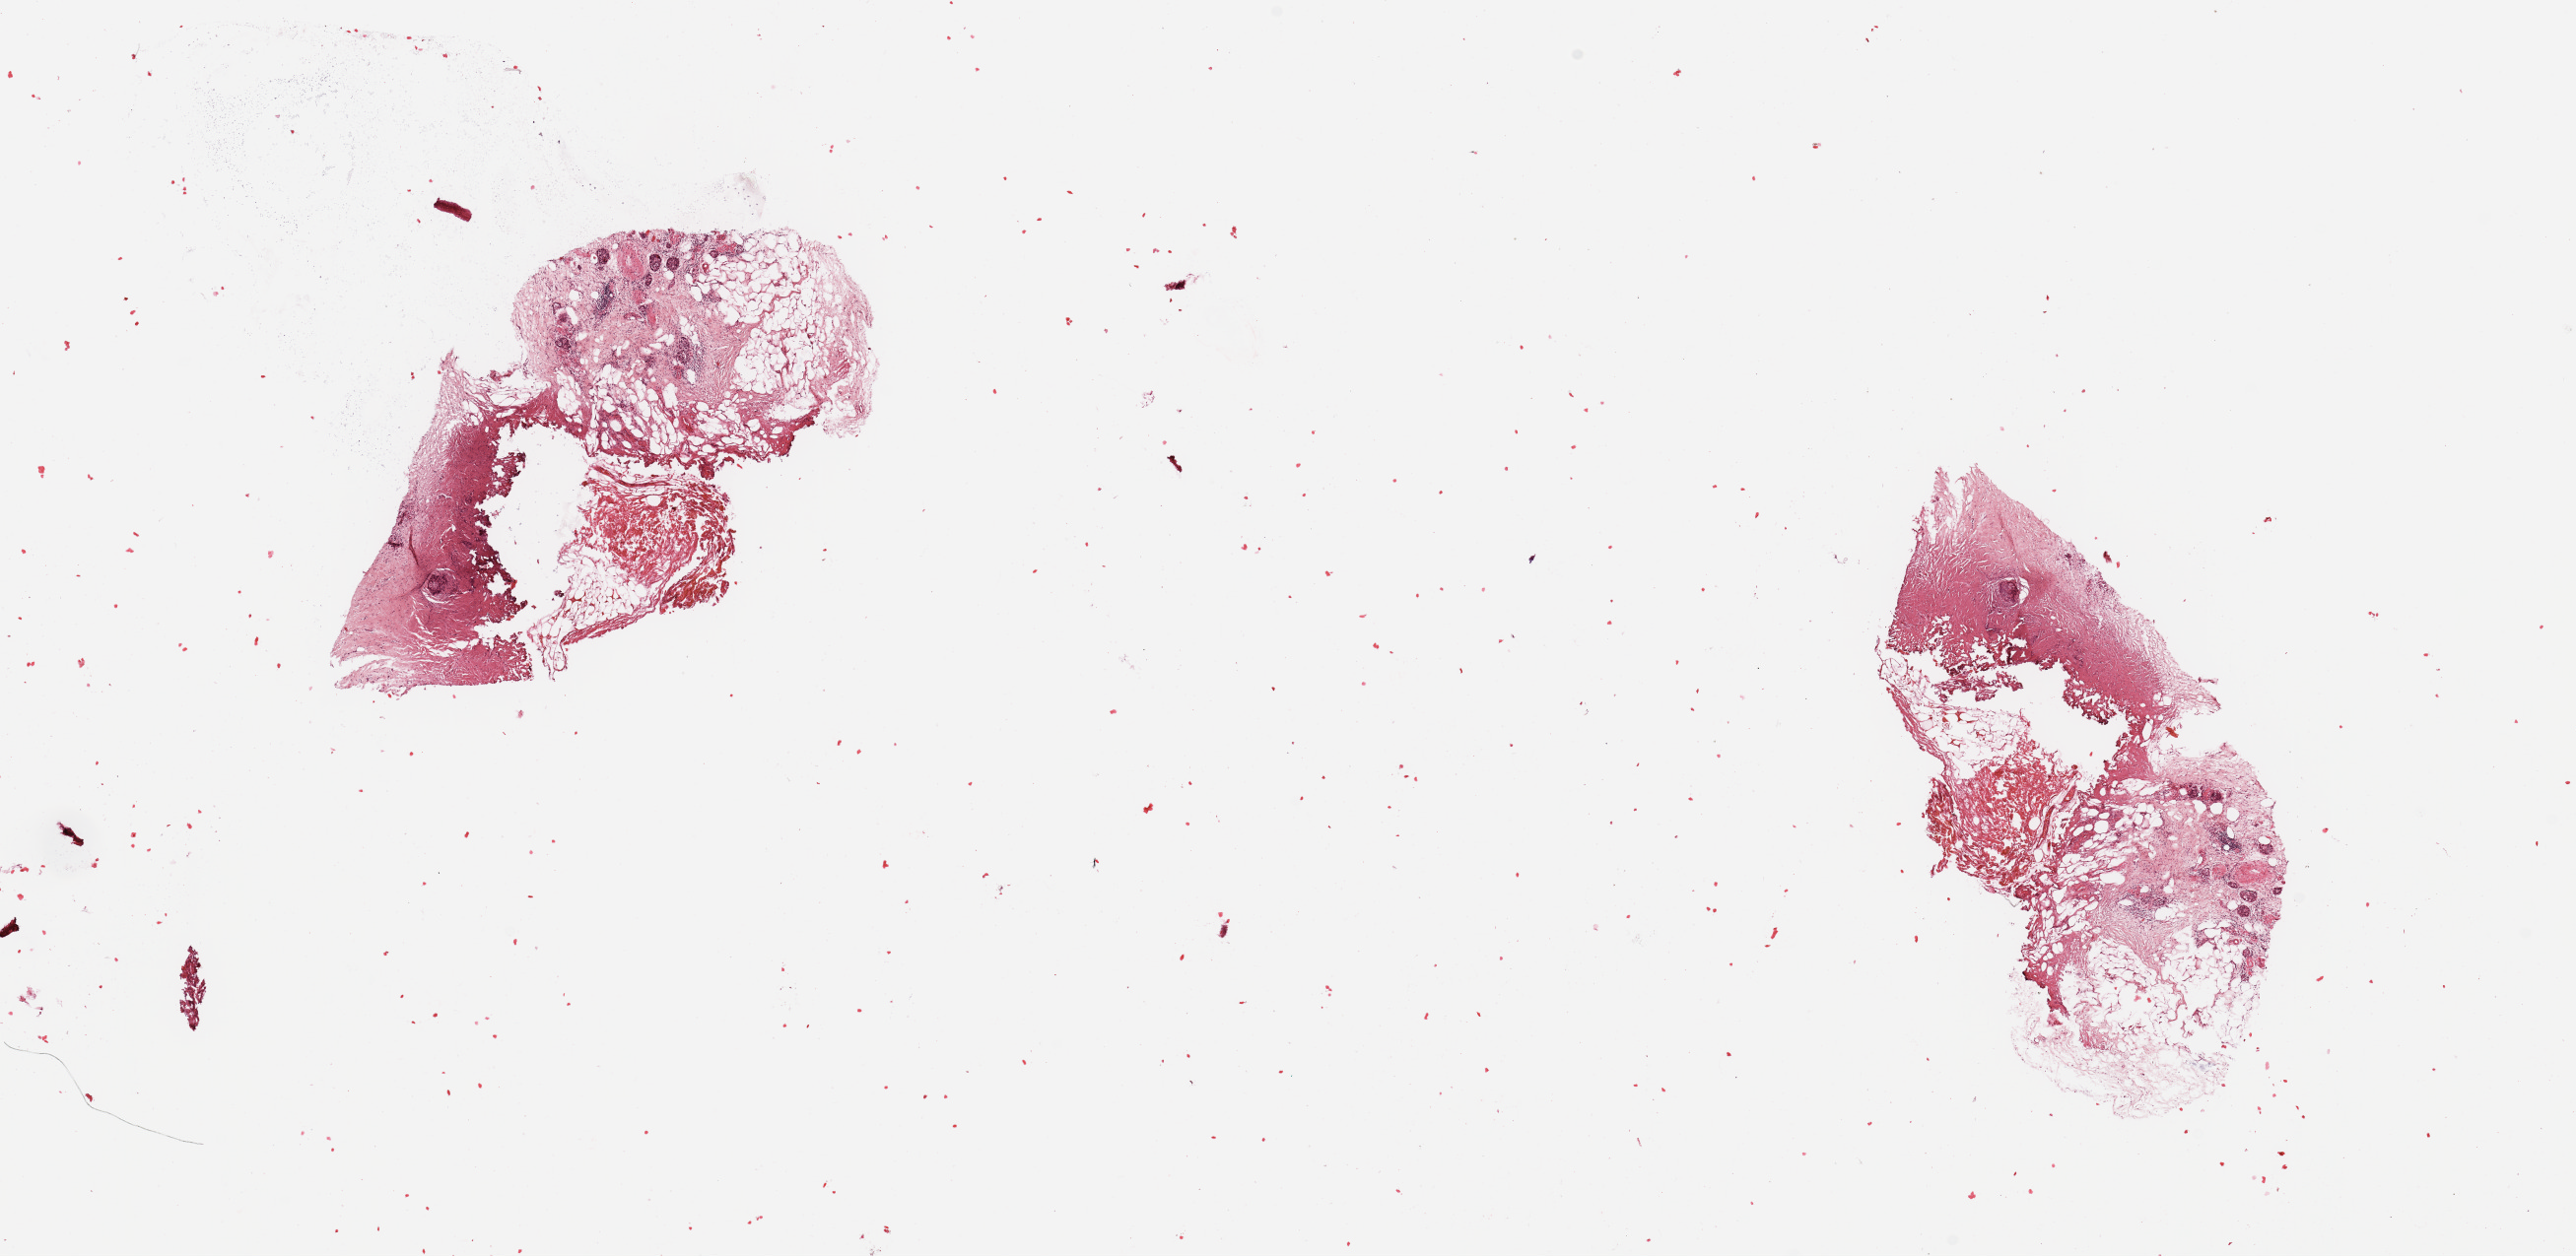
Whole-slide histology image, Hematoxylin and eosin (H&E) stained — shown as a low-resolution overview of the whole scanned area (about 20.7 x 10.1 mm), normal (non-tumour) tissue sample, sampled site: pancreas. 69-year-old male patient.
* this section: normal (non-tumour) tissue from the same patient
* patient diagnosis: Infiltrating duct carcinoma, NOS